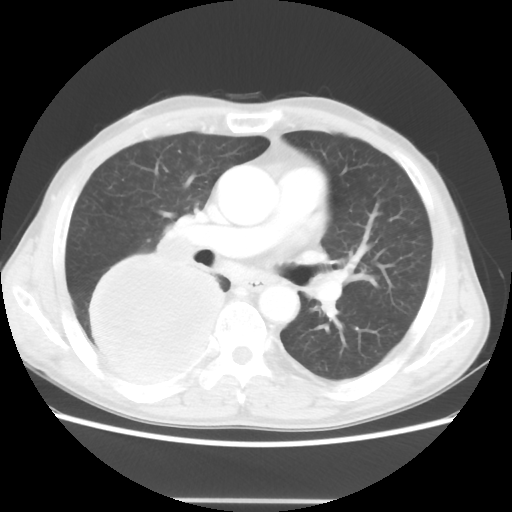
Chest CT, one axial slice; lung window (W 1500 / L -600 HU); 512 × 512 image matrix, field of view 361 × 361 mm. Male patient, age 66 years. From the clinical record (not read from this slice): clinical TNM (as recorded): T4 N1 M1.
Structures marked on this image (bounding box drawn by a radiologist):
- lung tumour (recorded histology: small cell carcinoma): bounding box (x1, y1, x2, y2) in pixels: (90, 253, 227, 393)